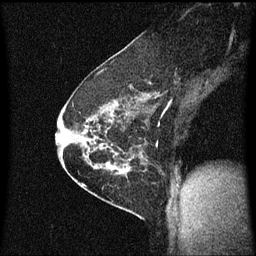
Breast MRI (dynamic contrast-enhanced), one sagittal slice. Position 40 of 60 along the scan axis. Dynamic contrast-enhanced series, image 2 of 3 at this slice position (ordered by acquisition). 1.5 T. TE 4.2 ms, TR 8.4 ms. 2 mm slice thickness. 256 × 256 image matrix. Female patient, age 60 years.
Annotated regions visible in this slice (semi-automatically segmented with operator editing):
- analysis volume of interest (the breast-tissue region the enhancement analysis was run in; not a lesion): bounding box [x1, y1, x2, y2] px = [69, 66, 148, 193]
- tumour enhancement mask (voxels above the 70 % enhancement threshold inside the analysis volume of interest): [69, 96, 147, 173]